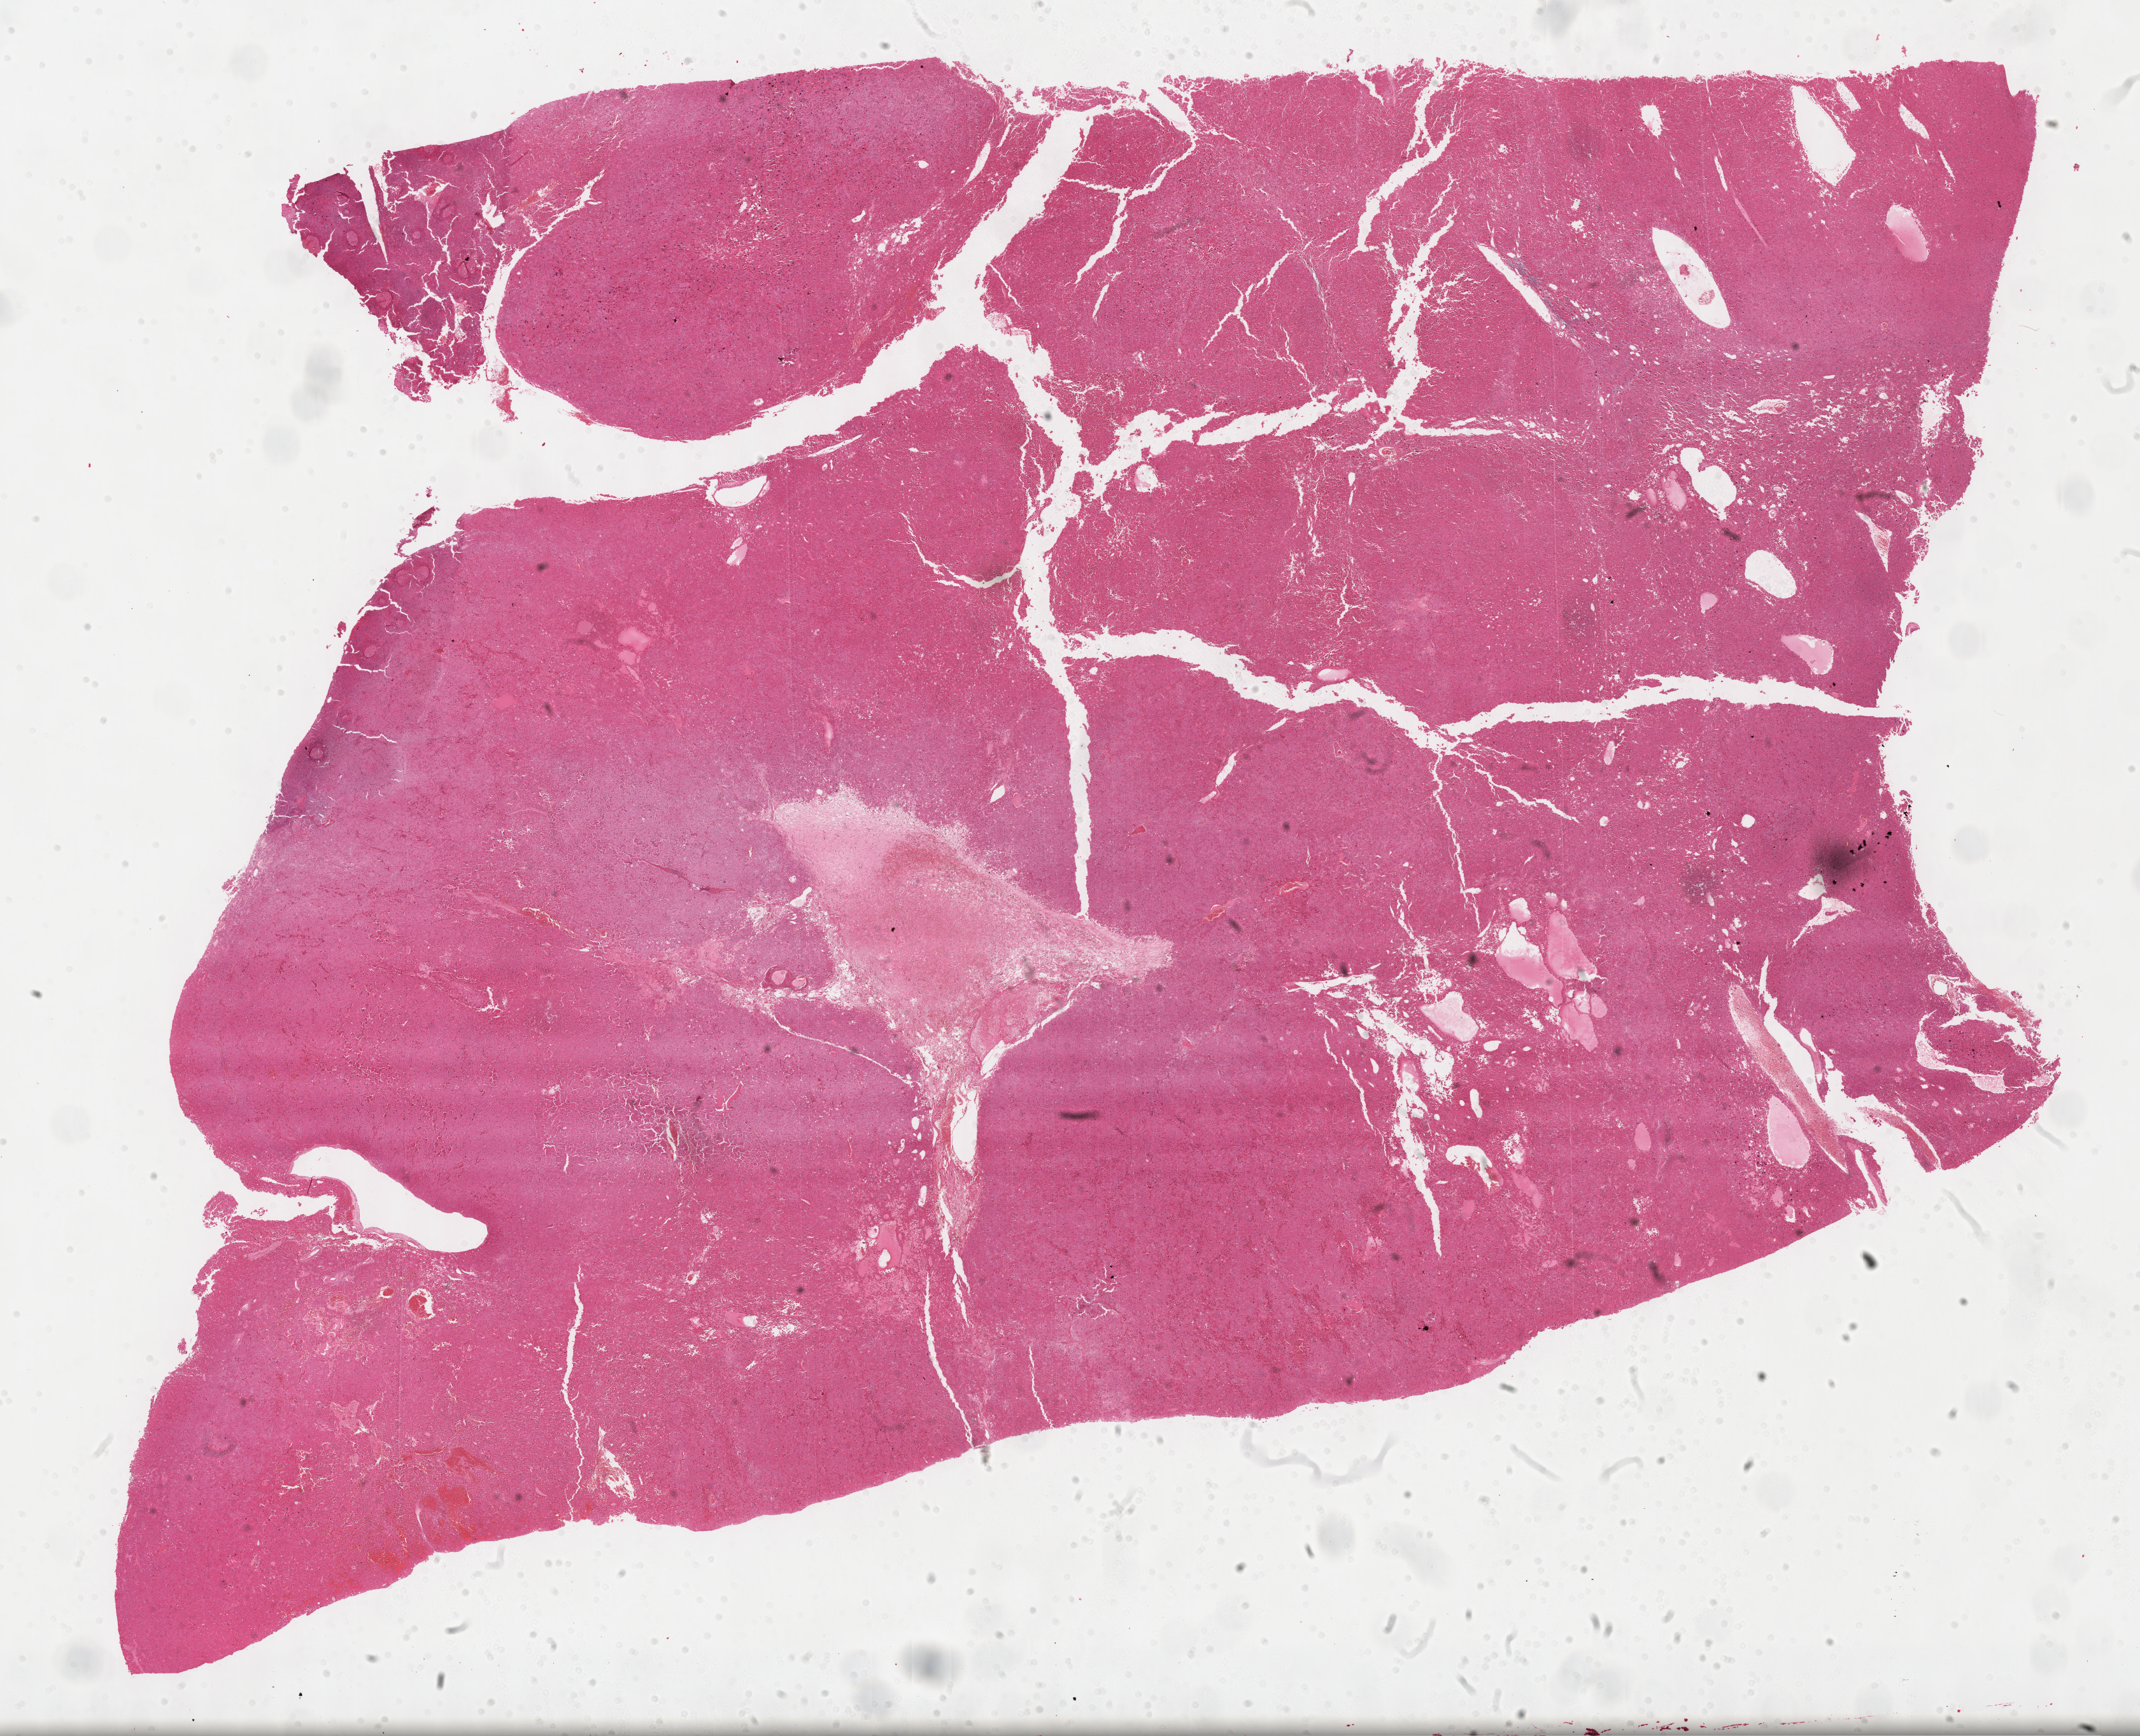
Whole-slide histology image, H&E-stained, low-resolution overview of the scanned area, about 27.2 x 22.1 mm. Formalin-fixed paraffin-embedded (FFPE) diagnostic section. Sample: primary tumour, adrenal cortex. Patient: female, age at initial diagnosis 57 years.
Laterality: left. Diagnosis: Adrenal cortical carcinoma (cortex of adrenal gland).